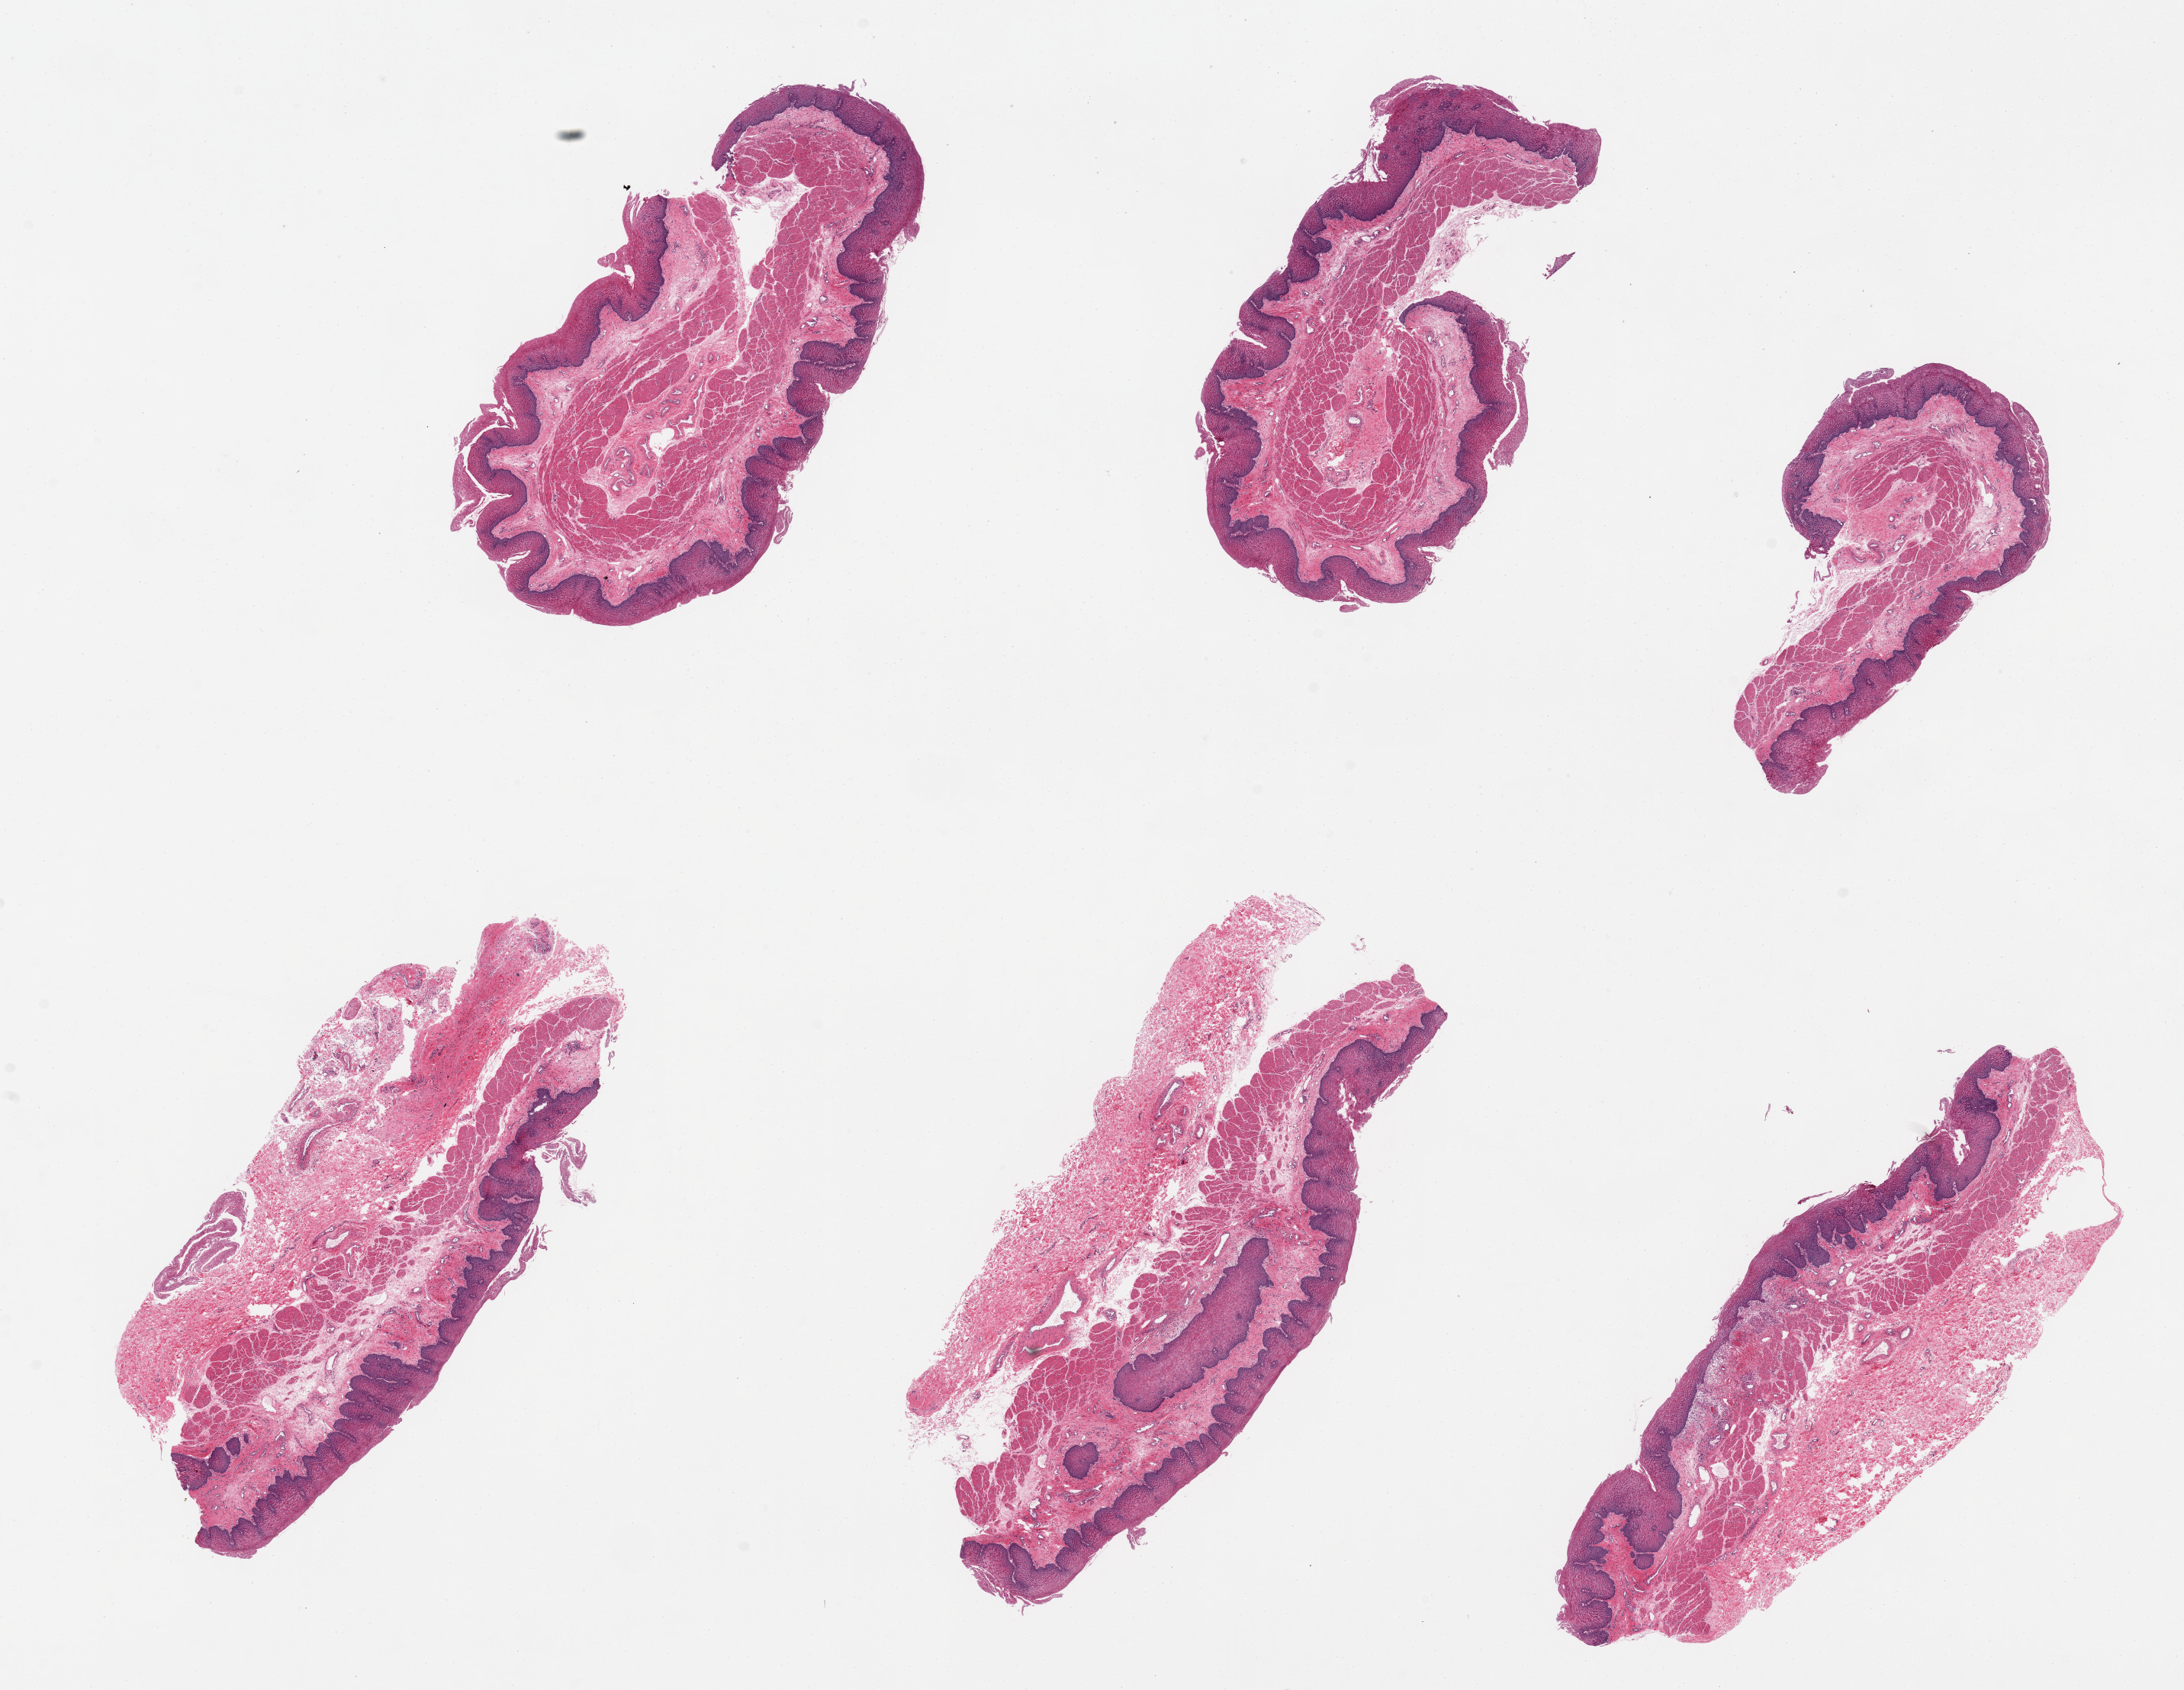
Digitized hematoxylin and eosin (H&E)-stained section, whole scanned area (about 22.6 x 17.5 mm, slide scanned at 20x) shown as a low-resolution overview; PAXgene-fixed paraffin-embedded (PFPE) section; section of esophageal mucous membrane (target tissue); tissue donor sample.
• reviewer comment on this tissue sample: 1 piece, 10x2.5 mm. Focal surface desquamation